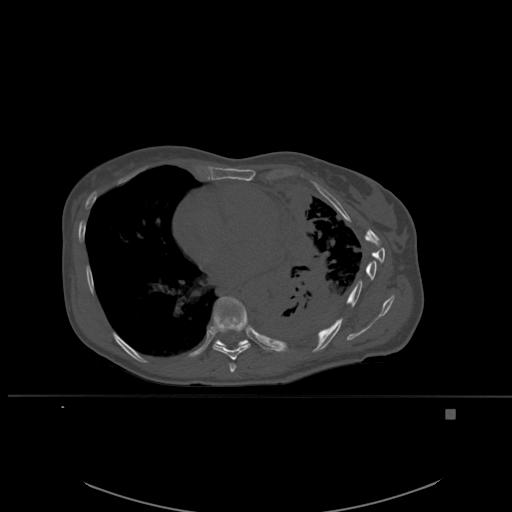
CT including the spine, one axial slice. Position 346 of 537 along the scan axis. Bone window (W 1800 / L 400 HU). 1.5 mm slice thickness. 512 × 512 image matrix, field of view 440 × 440 mm. Female patient, age 45 years. Case-level facts recorded for this patient, not image findings: primary cancer: lung.
Annotated regions visible in this slice (semi-automatically segmented with operator editing):
- T7 vertebra: bounding box (x1, y1, x2, y2) in pixels: (229, 363, 236, 373)
- T8 vertebra: (213, 316, 250, 360)
- T9 vertebra: (212, 297, 250, 349)